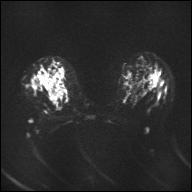
Breast MRI, one axial slice. Position 27 of 32 along the scan axis. Diffusion-weighted series; image 2 of 4 stored at this slice position (different b-values; order by instance number). 1.5 T. 192 × 192 image matrix, field of view 360 × 360 mm. Female patient.
Structures marked on this image (expert manual segmentation):
- tumour on diffusion-weighted imaging: box from (x=29, y=66) to (x=68, y=110) px